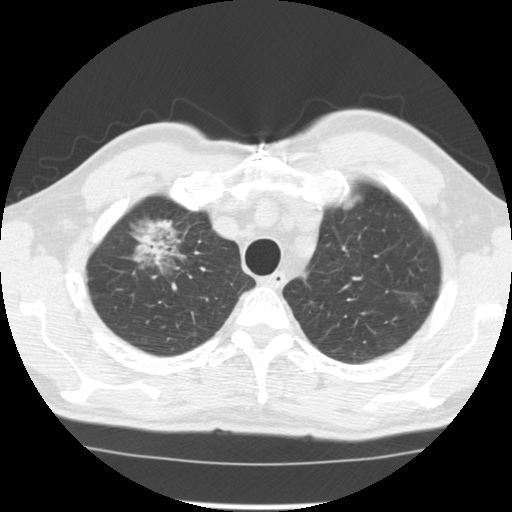
Low-dose screening chest CT, axial slice; third annual screen; lung window (W 1500 / L -600 HU); 120 kVp; slice 25 of 128 in the series; 512 × 512 image matrix. Male, age 64 years at enrolment. Former smoker at enrolment.
Expert-annotated lung lesion, box from (x=125, y=225) to (x=200, y=287) px. The screening reader recorded 3 non-calcified nodules or masses ≥4 mm on this exam; which of them this box marks is not recorded. Official screen result: positive, other. Later outcome: lung cancer diagnosed 30 days after this screen — adenocarcinoma, NOS, right upper lobe, well differentiated (G1), stage IB (AJCC 6th edition), 45 mm at pathology.